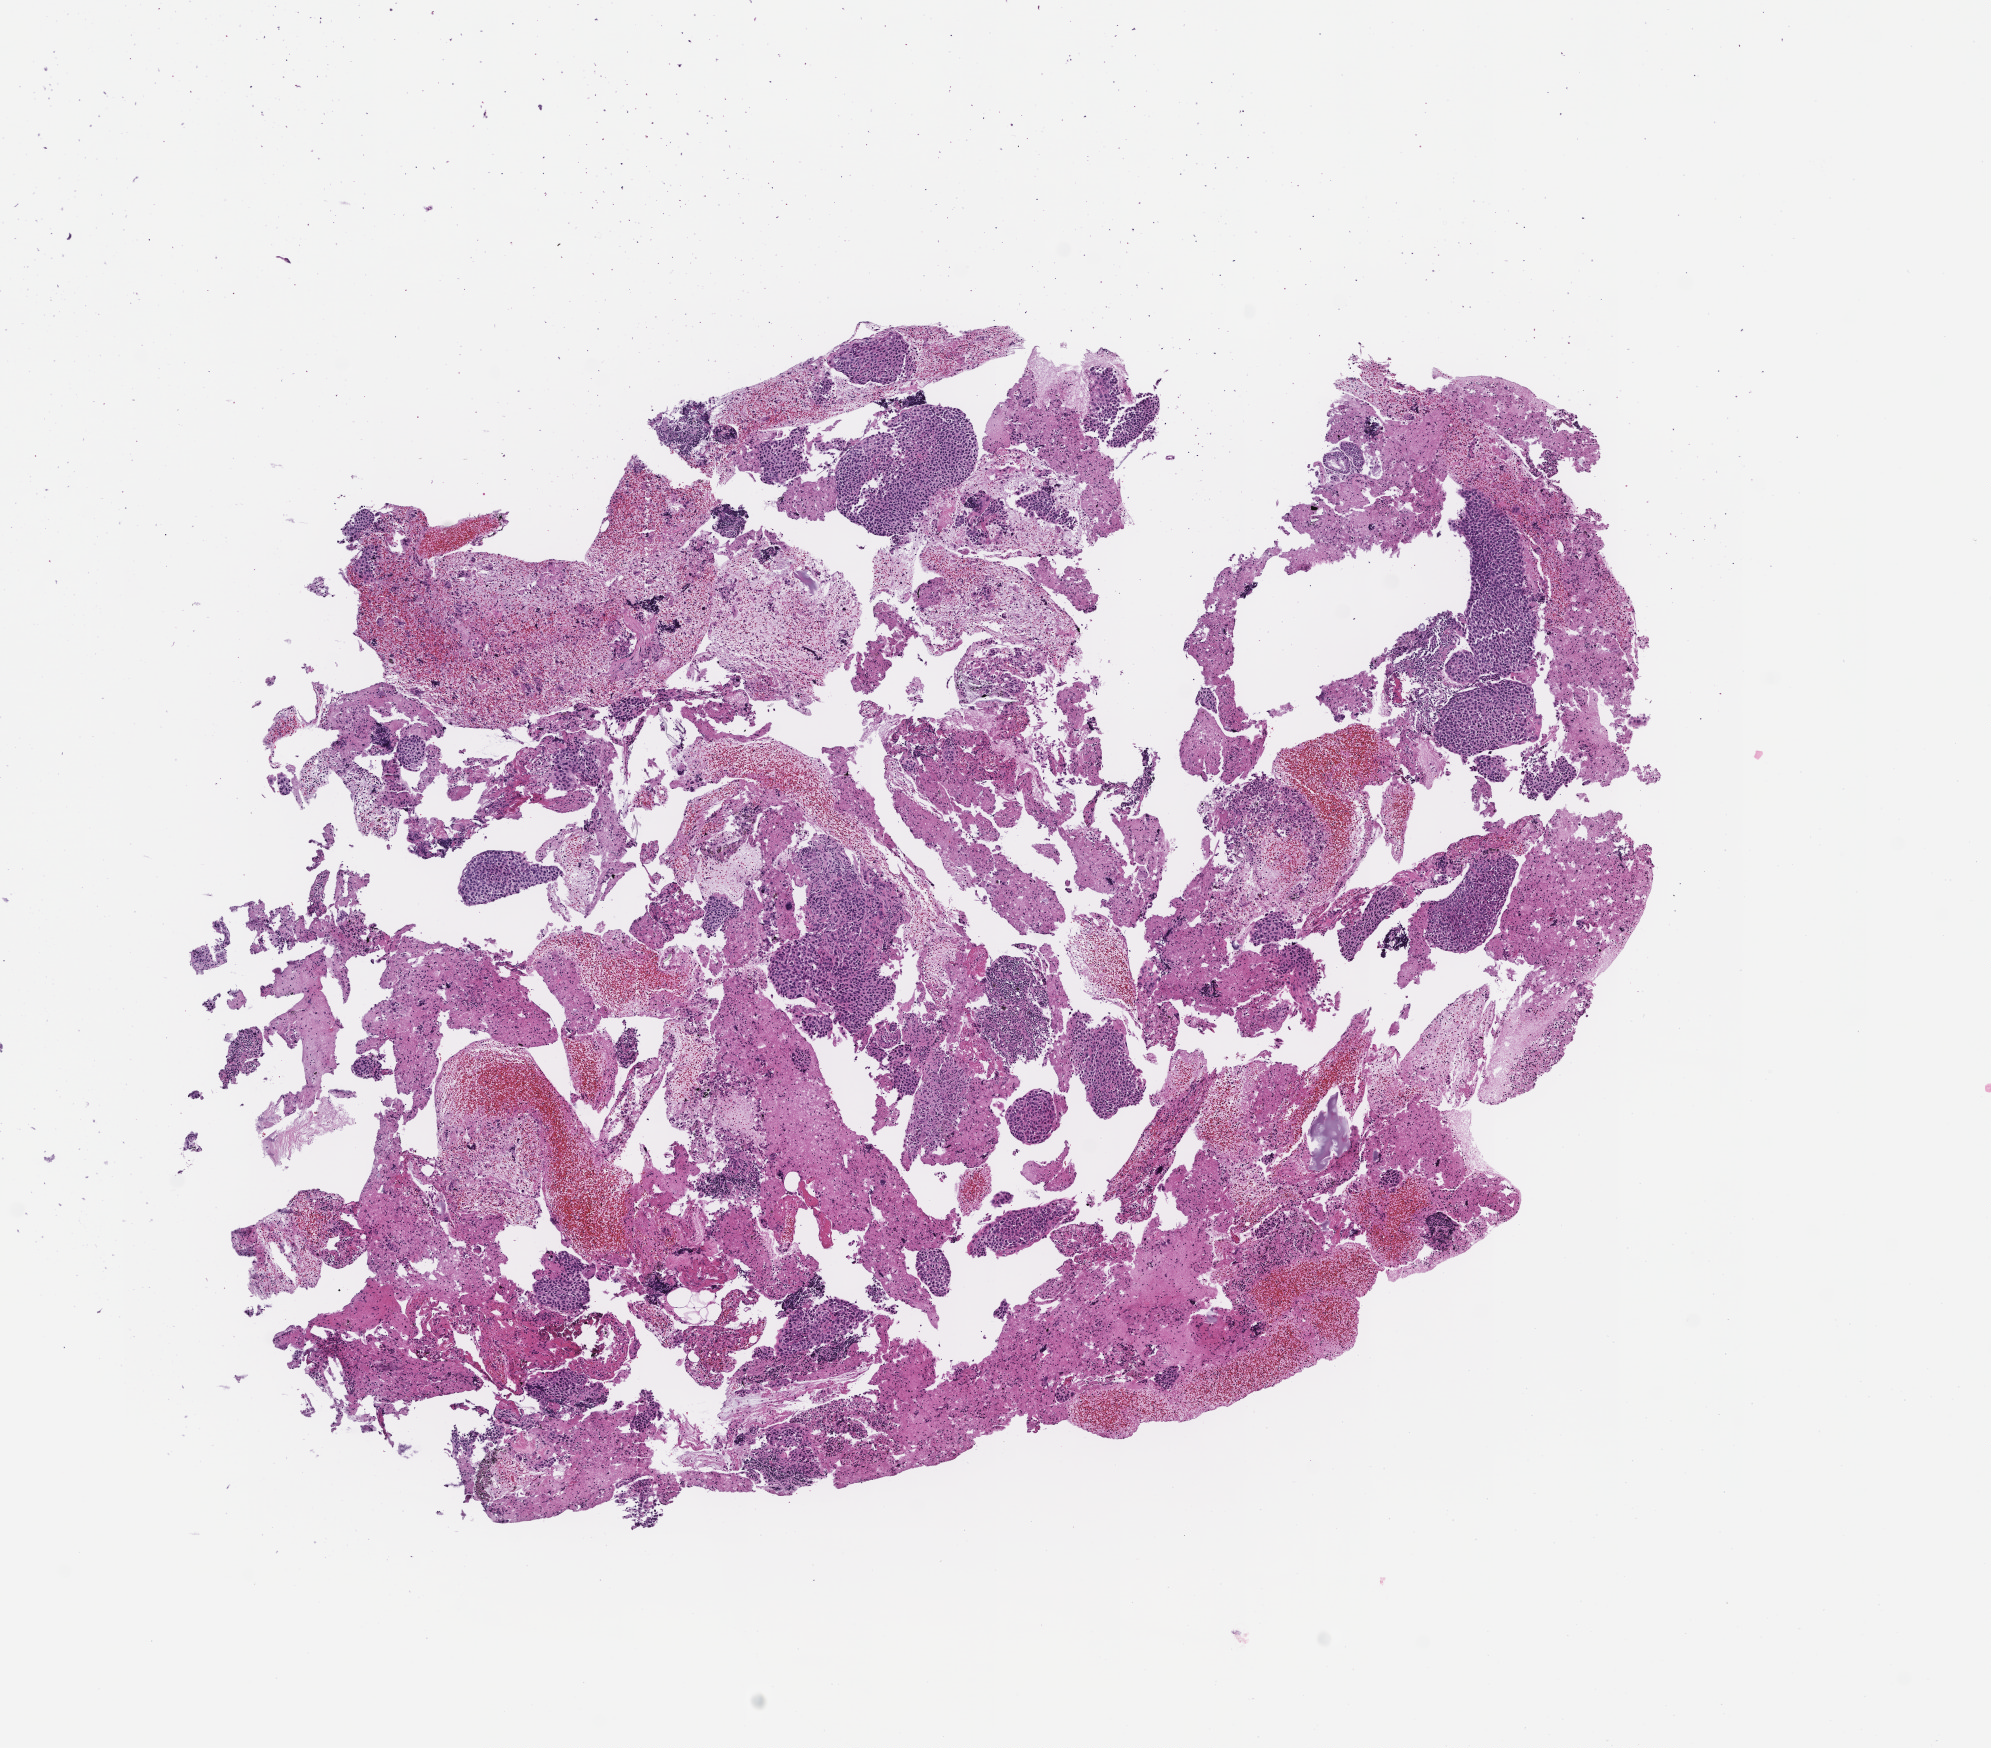
Whole-slide image, haematoxylin and eosin stain, low-resolution overview of the scanned area, about 8.0 x 7.1 mm, formalin-fixed paraffin-embedded section, site: lung, specimen time point: archival tissue. Male patient.
* this section: primary tumor
* diagnosis: Non-Small Cell Lung Carcinoma